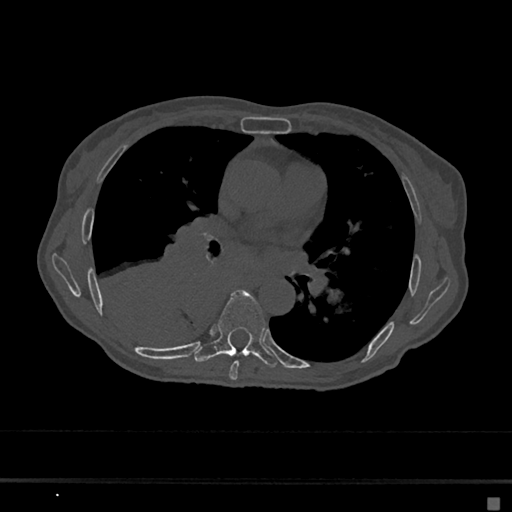
CT including the spine, one axial slice; reconstruction kernel Br40s/3; bone window (W 1800 / L 400 HU); 0.5 mm slice thickness; 512 × 512 image matrix, field of view 360 × 360 mm. Patient: female, 68 years. From the clinical record (not read from this slice): primary cancer: renal.
Outlined on this slice (semi-automatic segmentation, software-assisted and operator-edited):
- T6 vertebra: bounding box [x1, y1, x2, y2] px = [229, 361, 239, 380]
- T7 vertebra: [194, 291, 277, 367]